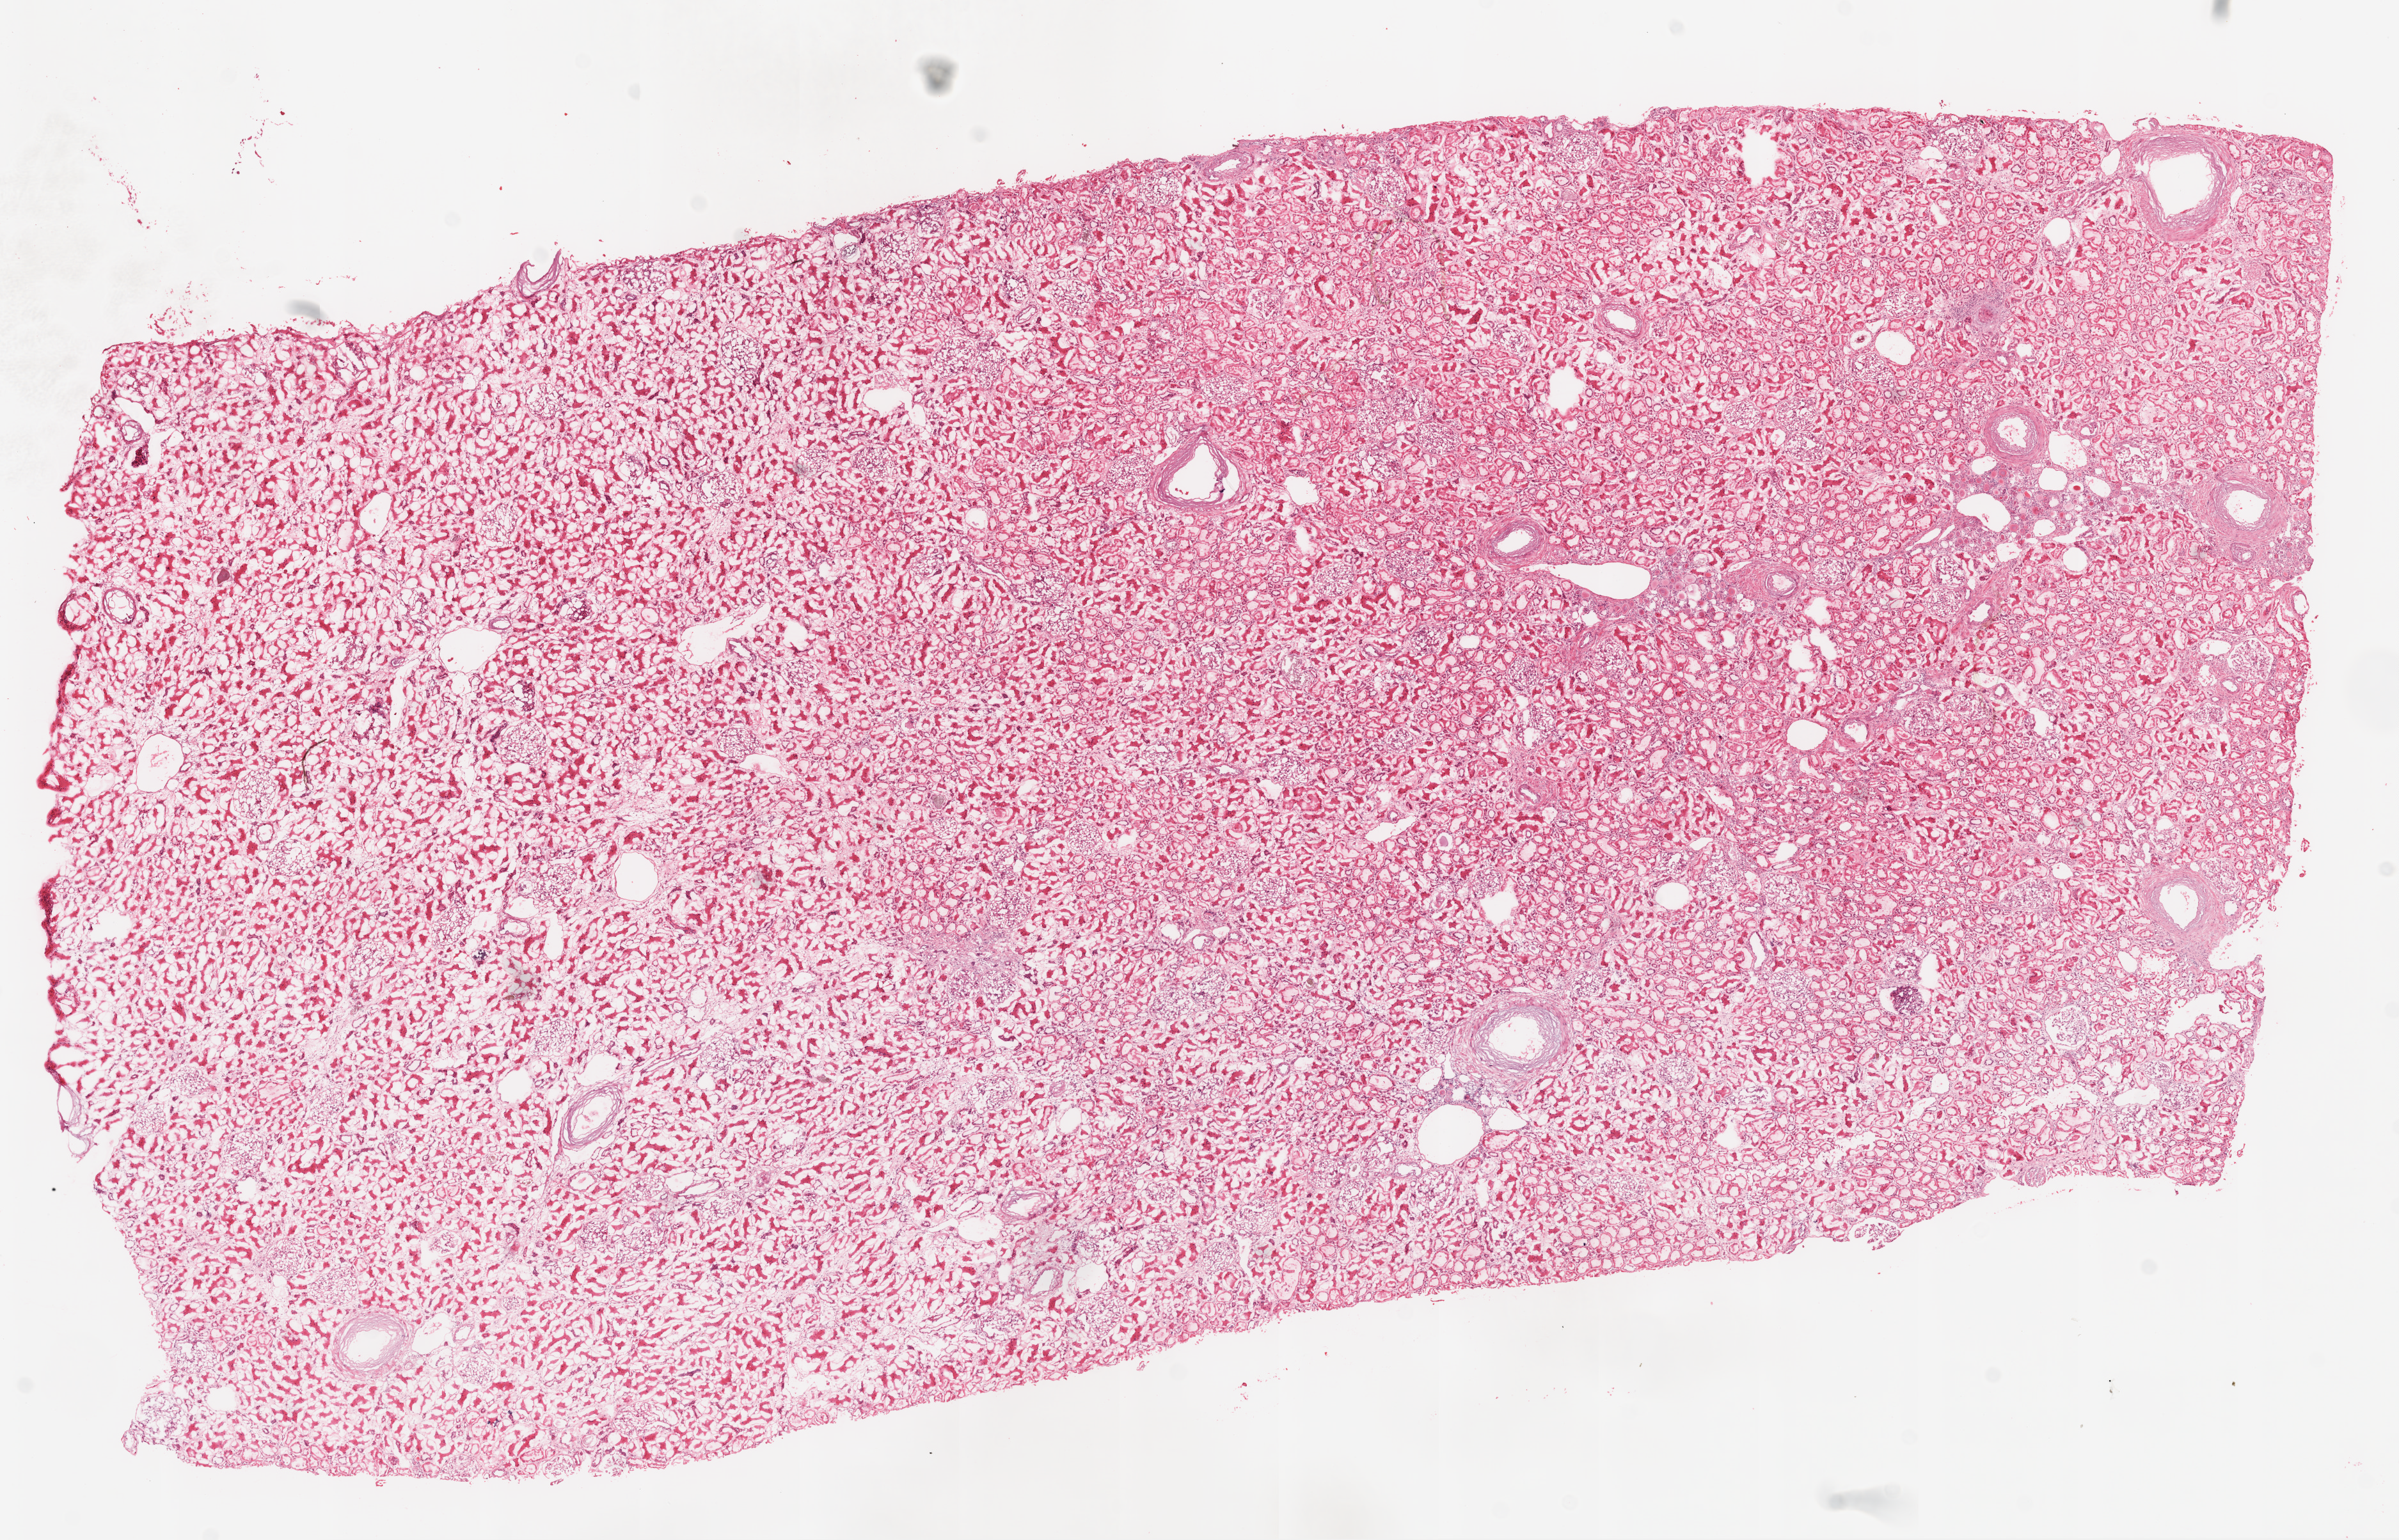
Digitized H&E tissue section (whole slide), shown as a low-resolution overview of the whole scanned area (about 15.0 x 9.7 mm, acquisition: 20x scan), frozen section from the top of the tissue portion, solid tissue normal (non-tumour tissue) sample from the kidney. Patient: male, age at initial diagnosis 74 years.
This section: solid tissue normal (non-tumour) sample from the same patient. Patient diagnosis: Clear cell adenocarcinoma, NOS.